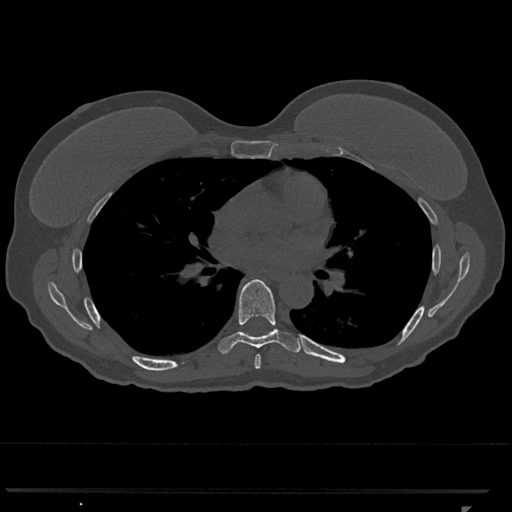
CT including the spine, one axial slice. Slice 717 of 793 in the series (ordered by position). 120 kVp. Bone window (W 1800 / L 400 HU). 0.5 mm slice thickness. 512 × 512 image matrix. Female patient, age 62 years. Case-level facts recorded for this patient, not image findings: primary cancer: renal.
Annotated regions visible in this slice (semi-automatic segmentation, software-assisted and operator-edited):
- T6 vertebra: bounding box <254,354,261,369> (left, top, right, bottom; pixels)
- T7 vertebra: <218,279,301,354>